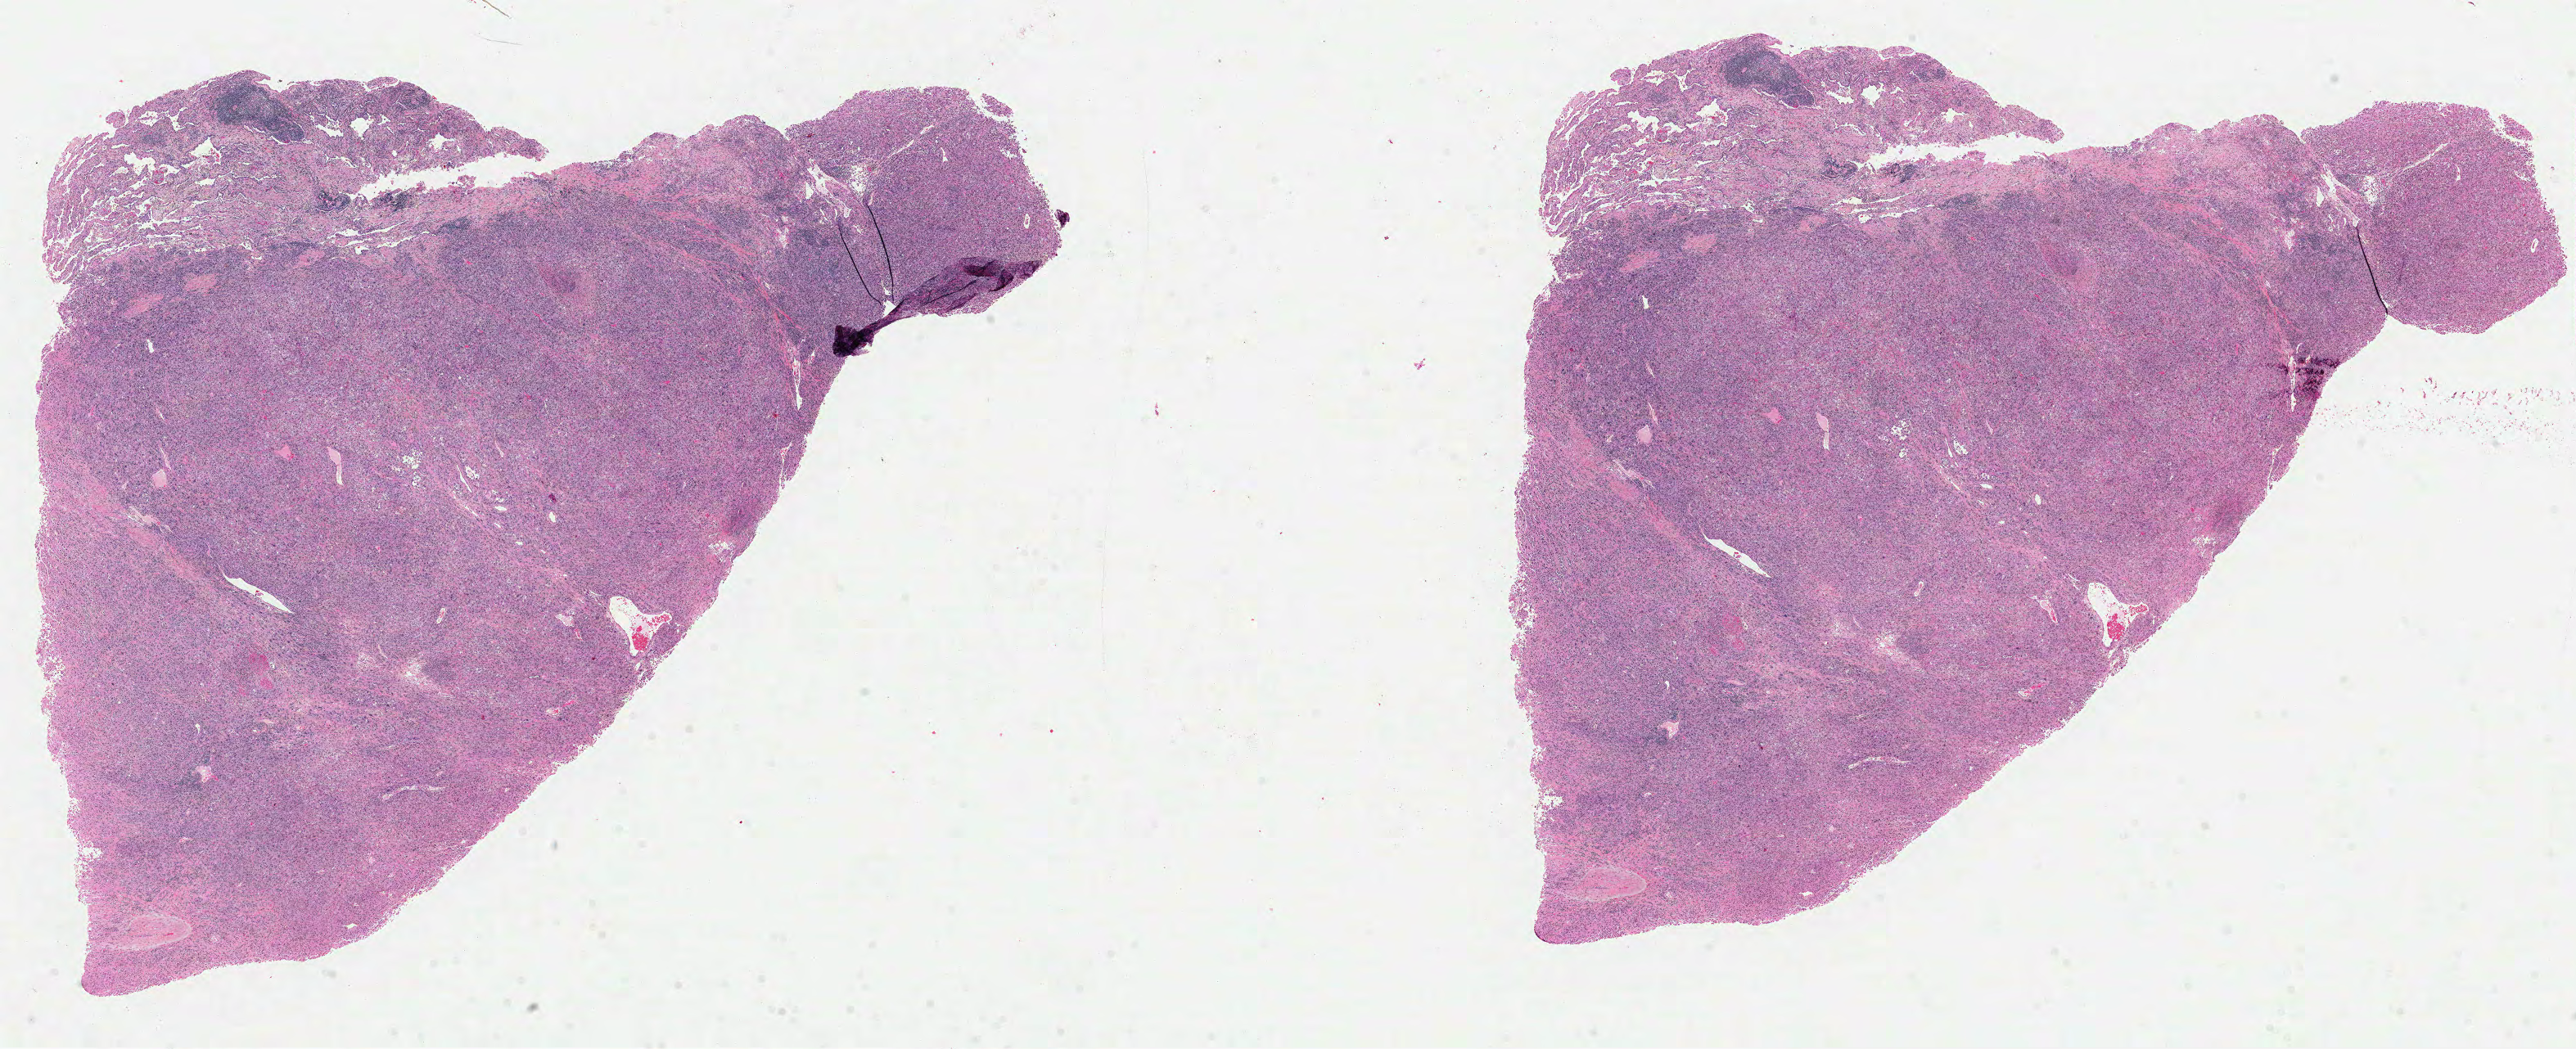
H&E whole-slide image, low-resolution overview of the scanned area, about 25.4 x 10.3 mm (acquisition: 40x scan). Formalin-fixed paraffin-embedded (FFPE) diagnostic section. Sample: primary tumour, lung. Patient: female, age at initial diagnosis 66 years.
• laterality: right
• pathologic diagnosis: Adenocarcinoma, NOS (upper lobe, lung)
• AJCC pathologic stage: IB (5th edition)